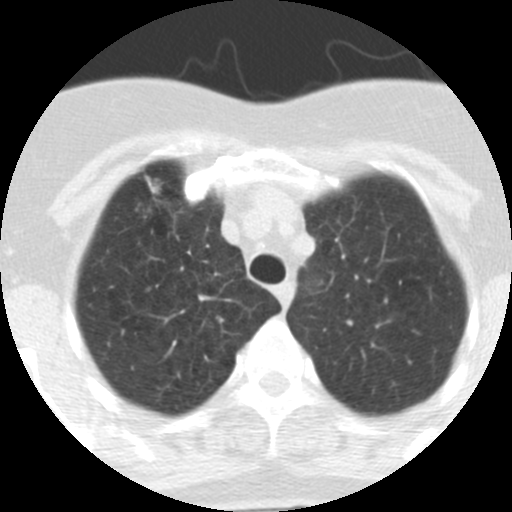
Low-dose screening chest CT, one axial slice; slice 255 of 313 in the series (ordered by position); 120 kVp; lung window (W 1500 / L -600 HU); 512 × 512 image matrix.
Annotated regions visible in this slice (outlined manually by an expert reader):
- lesion 1 (tumor, upper lobe of right lung): bounding box <145,176,159,193> (left, top, right, bottom; pixels)